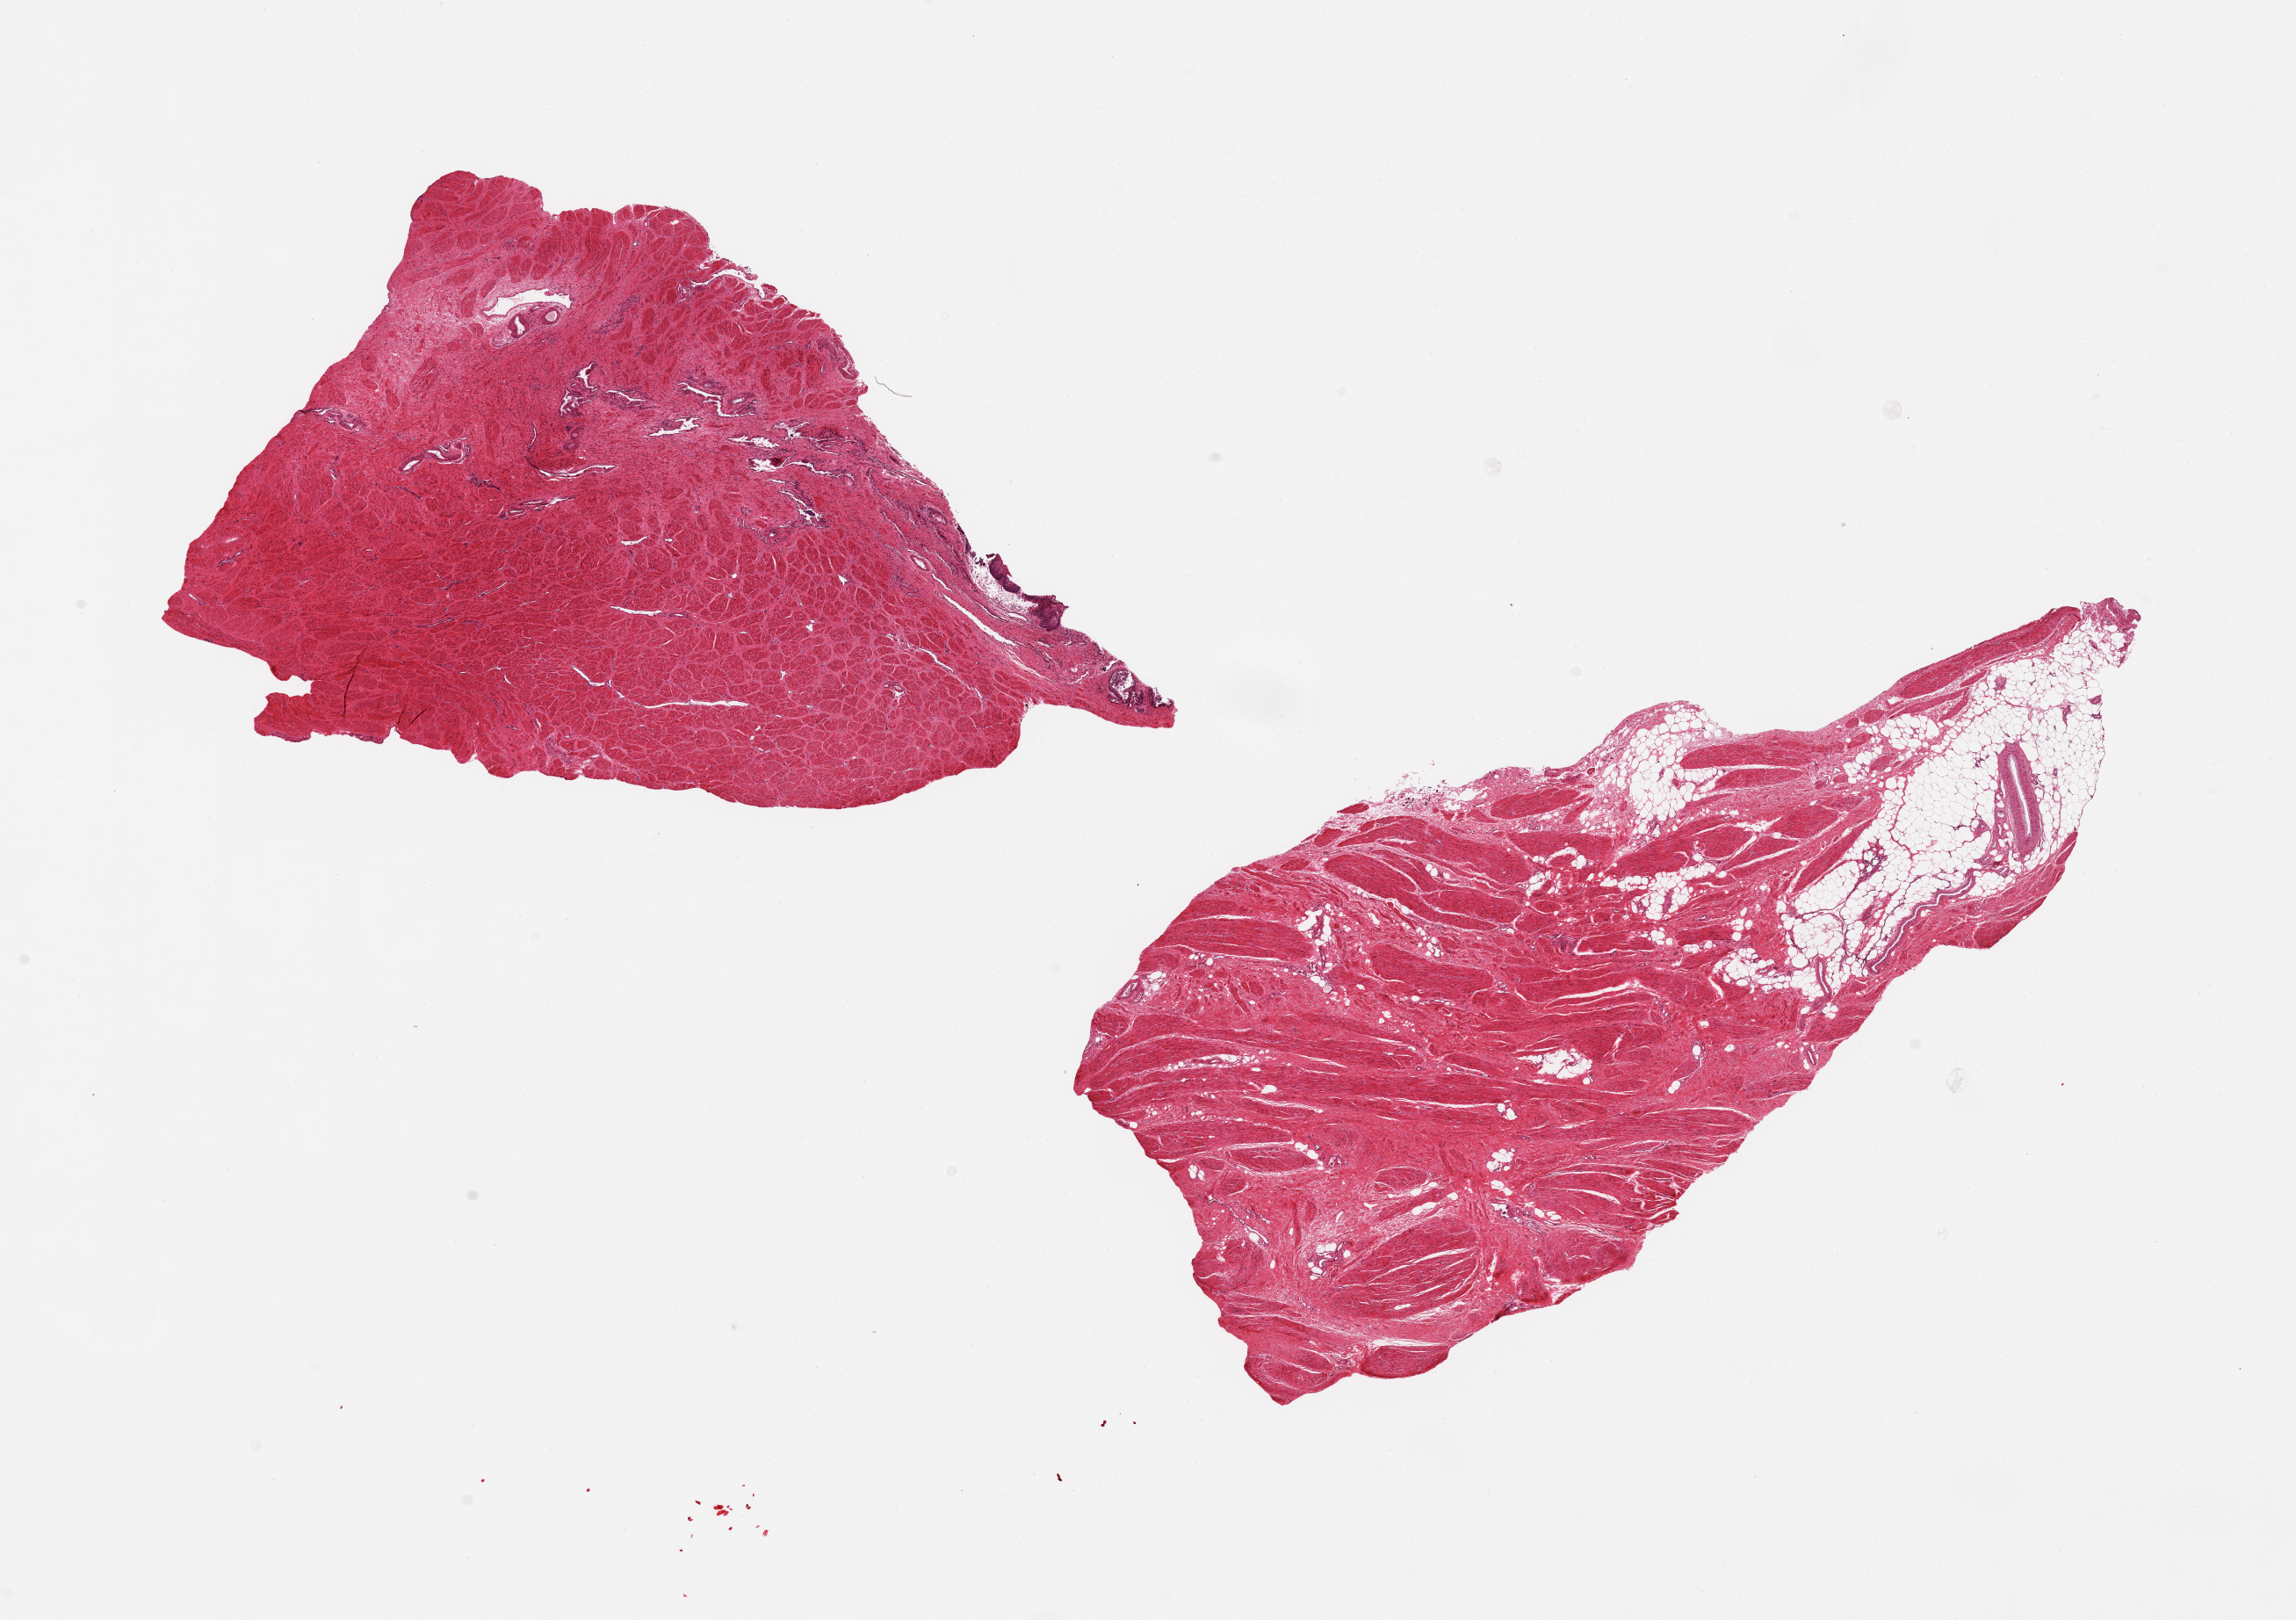
Hematoxylin and eosin (H&E) whole-slide image, a low-resolution overview of the entire scanned area, about 20.7 x 14.6 mm (from a 20x scan), PAXgene-fixed paraffin-embedded (PFPE) section, target tissue: prostate, donor tissue sample. Donor: male.
Review note (as recorded): 2 pieces ~7x6mm. Largely peripheral stroma/fat, adherent smooth muscle, minimal autolyzed glandular elements.